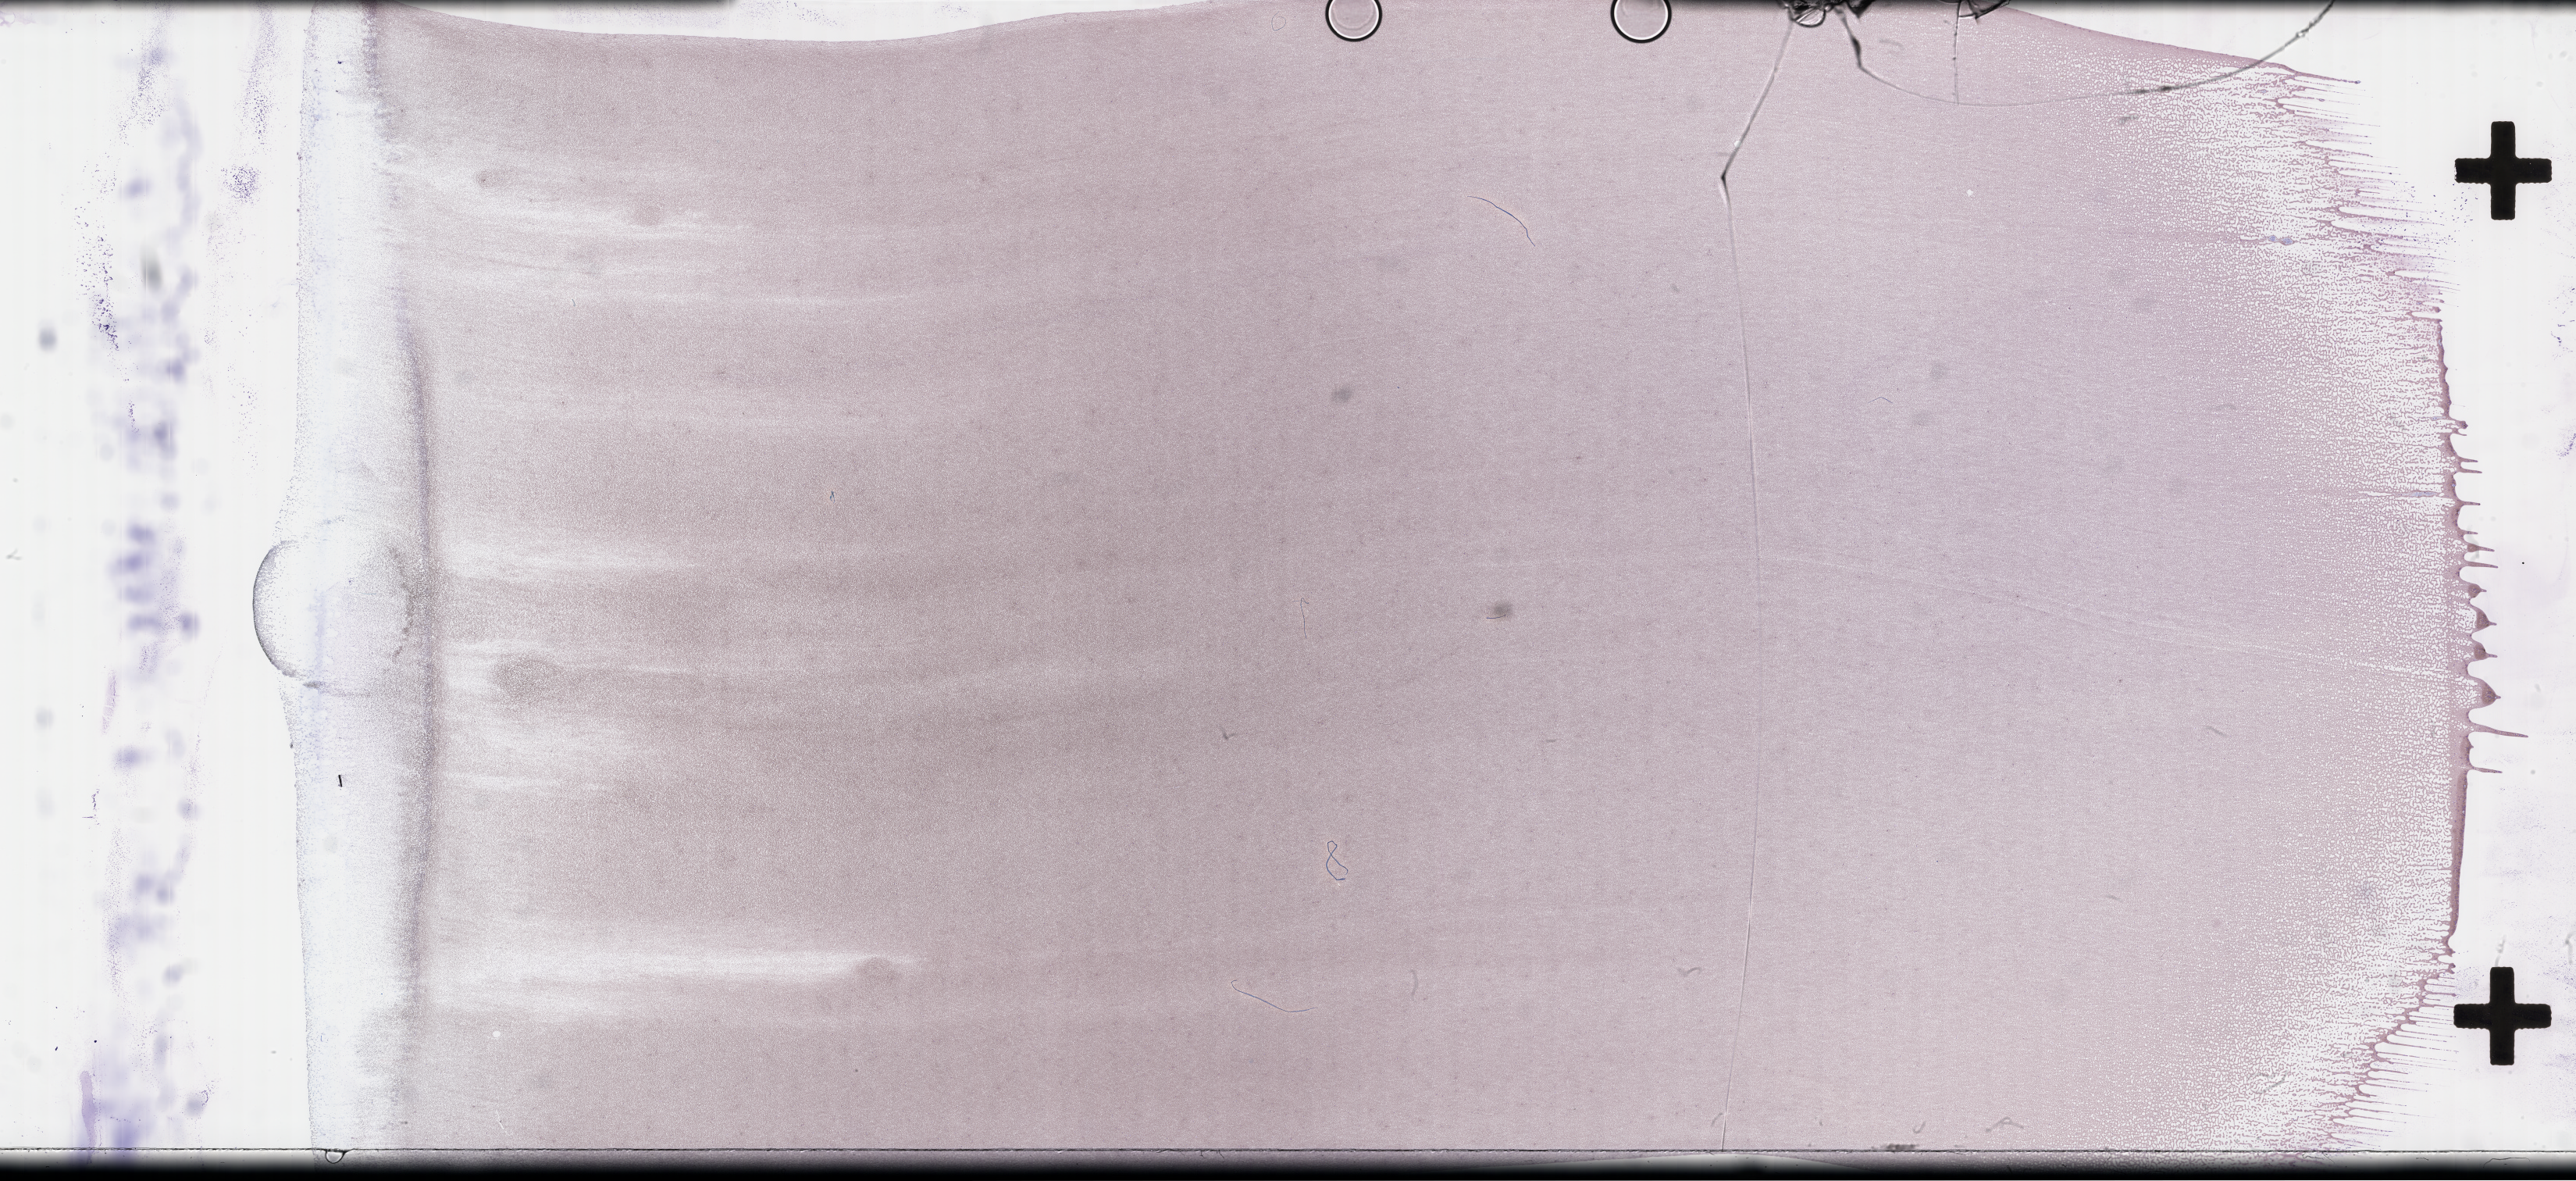
Whole-slide image of a whole blood smear, Wright-Giemsa stain — shown as a low-resolution overview of the whole scanned area (about 53.3 x 24.4 mm); collected on treatment. Male patient.
* from a patient with: Plasma Cell Myeloma